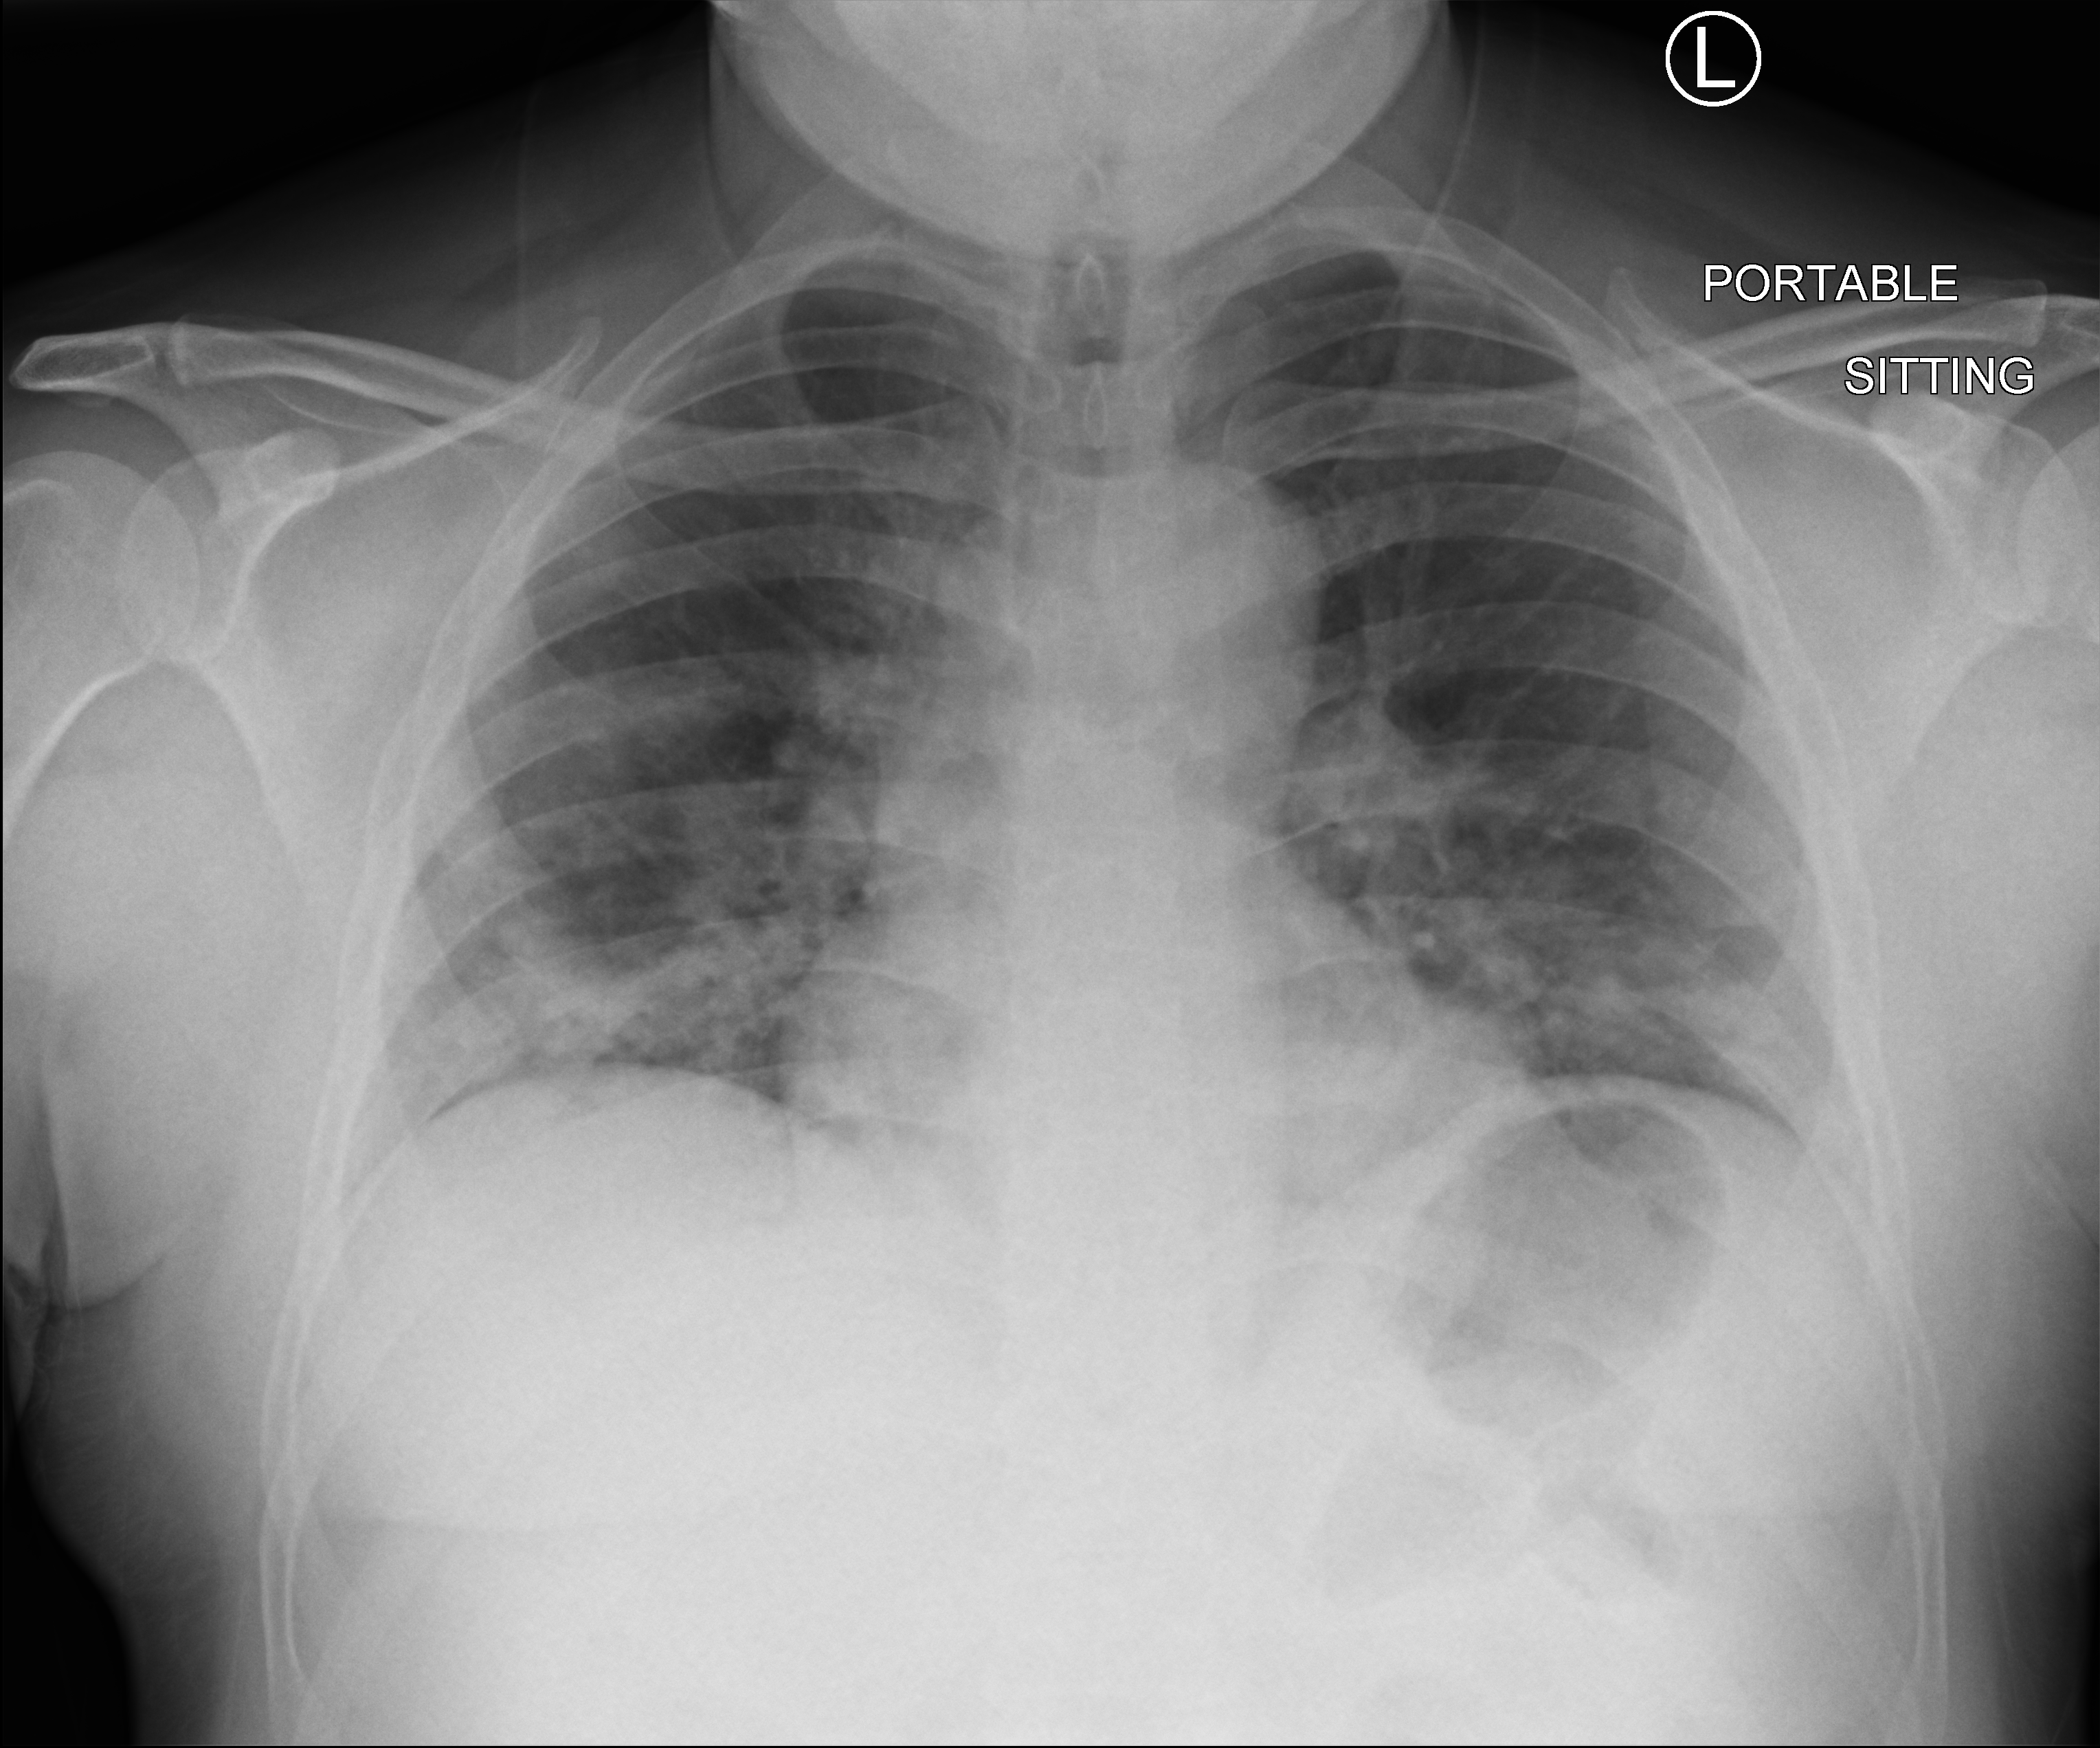
Chest X-ray (portable), anteroposterior (AP) projection. Patient hospitalised with COVID-19; male, aged 18–59 years.
Hospital-stay facts (about this admission, not read from this image; timing relative to this image not recorded): mechanically ventilated during this hospital stay: no.